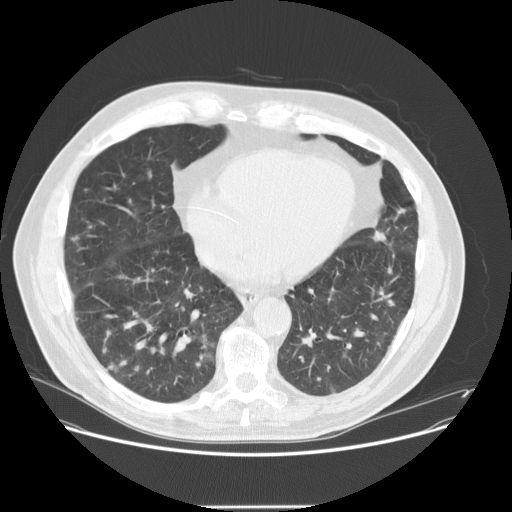
Low-dose screening chest CT, one axial slice; position 55 of 143 along the scan axis; 120 kVp; lung window (W 1500 / L -600 HU); 512 × 512 image matrix, field of view 400 × 400 mm.
Structures marked on this image (expert manual segmentation):
- lesion 1 (tumor, lower lobe of right lung): bounding box (x1, y1, x2, y2) in pixels: (204, 353, 212, 357)